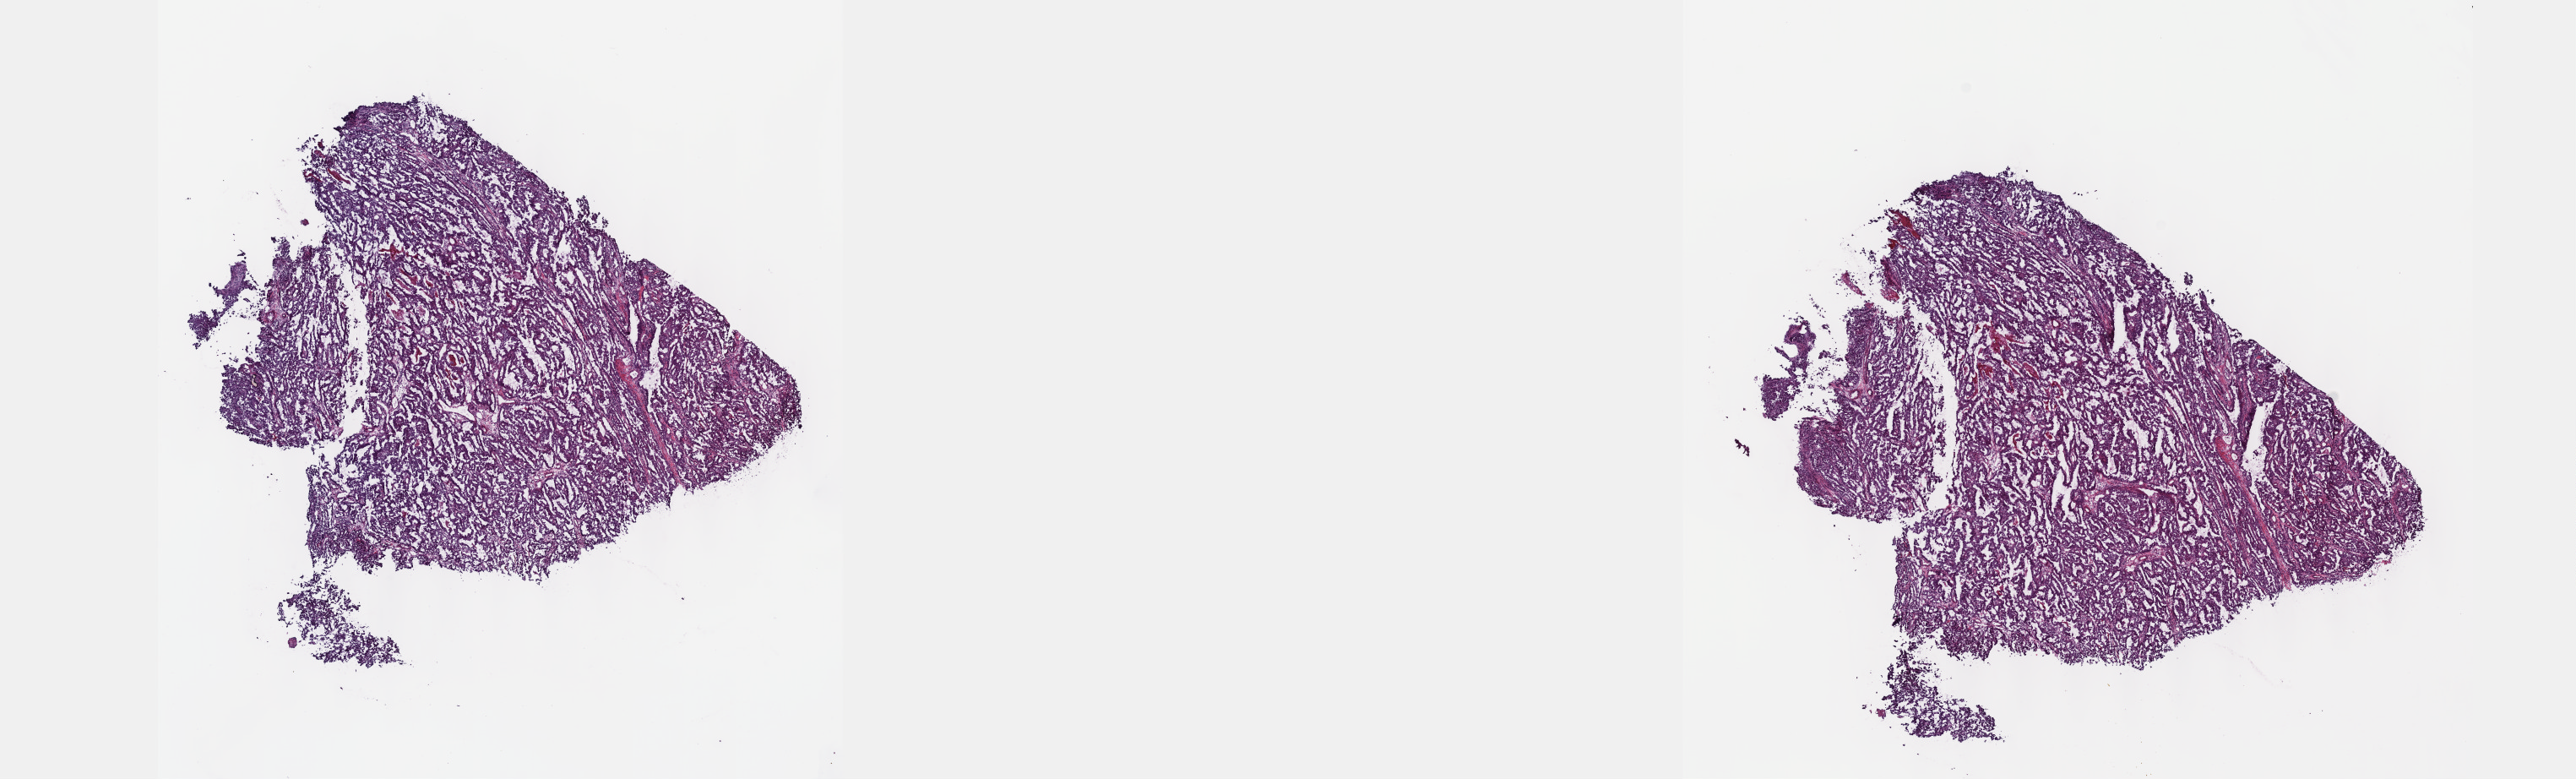
H&E whole-slide image, whole scanned area (about 24.6 x 7.5 mm, slide scanned at 40x) shown as a low-resolution overview. Frozen section. Kidney, primary tumour sample. Female, age 38 years at initial diagnosis. Composition of this section per pathologist review: tumour cells 90%, tumour nuclei 95%, normal cells 0%, stromal cells 10%, necrosis 0%. Infiltration values recorded for this section: lymphocyte infiltration 0%, monocyte infiltration 0%, neutrophil infiltration 0%.
Lymph nodes positive (case pathology): 3 of 3 examined. AJCC pathologic stage: IV (7th edition). Histologic diagnosis: Papillary adenocarcinoma, NOS.